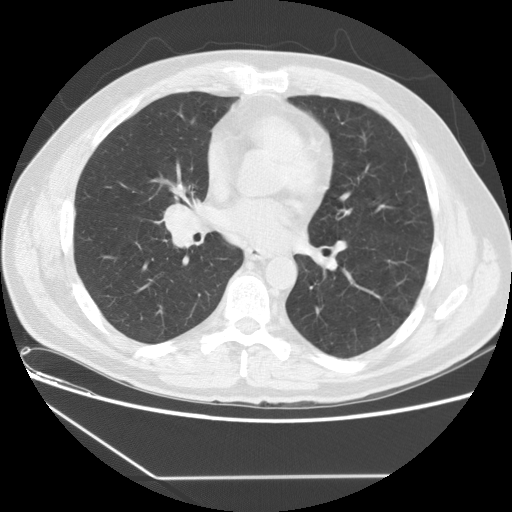
Low-dose screening chest CT, one axial slice; position 72 of 154 along the scan axis; 120 kVp; lung window (W 1500 / L -600 HU); 2.5 mm slice thickness; 512 × 512 image matrix.
Outlined on this slice (expert manual segmentation):
- lesion 1 (tumor, middle lobe of right lung): bounding box [x1, y1, x2, y2] px = [165, 204, 199, 235]